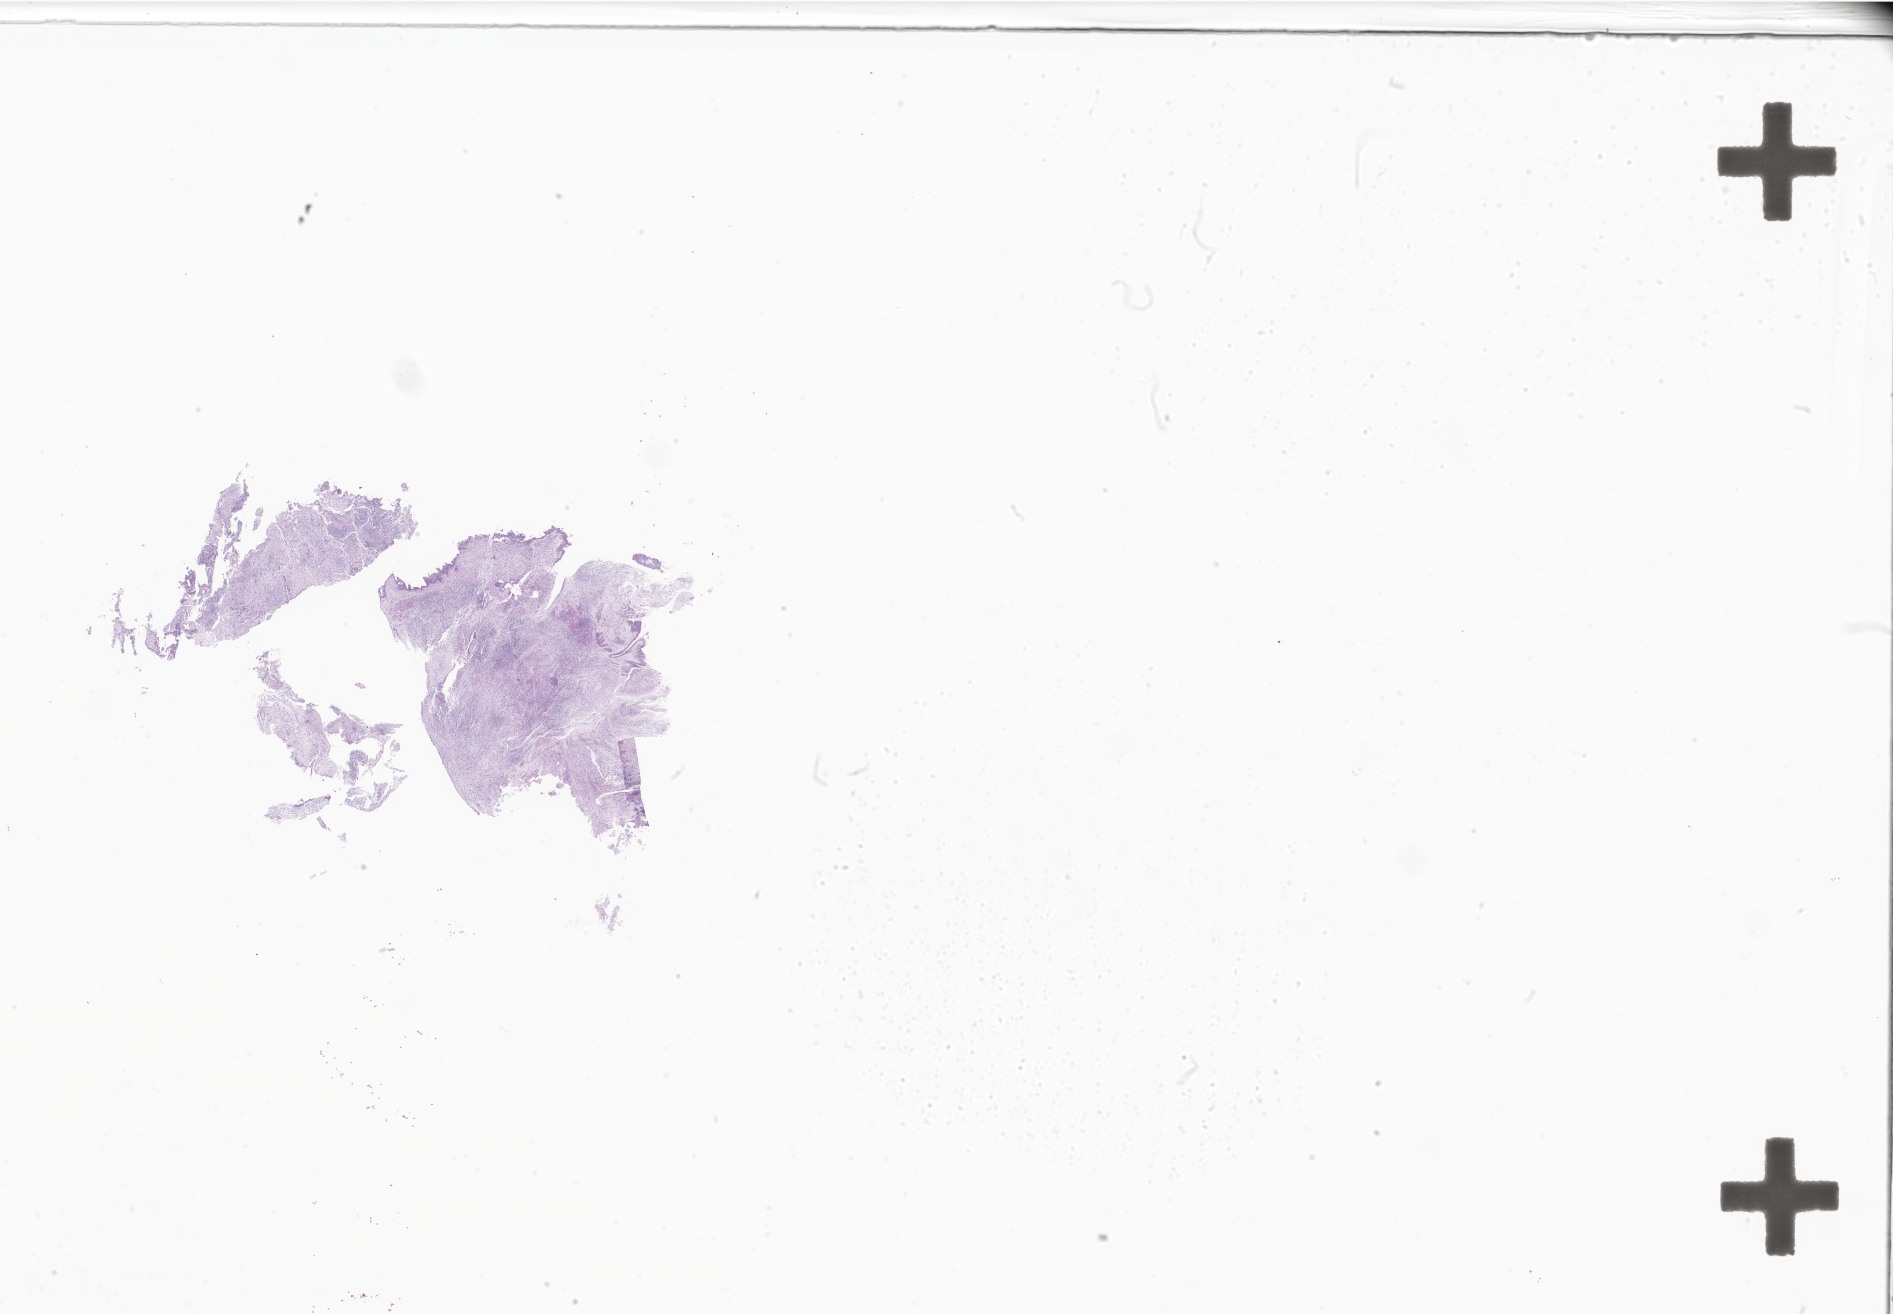
Haematoxylin and eosin whole-slide image of tumor tissue from the nasal cavity, whole scanned area (about 31.9 x 22.2 mm) shown as a low-resolution overview; formalin-fixed paraffin-embedded section. Female patient, age 54 months (4 years 6 months).
* diagnosis (ICD-O-3 morphology term): Embryonal rhabdomyosarcoma, NOS